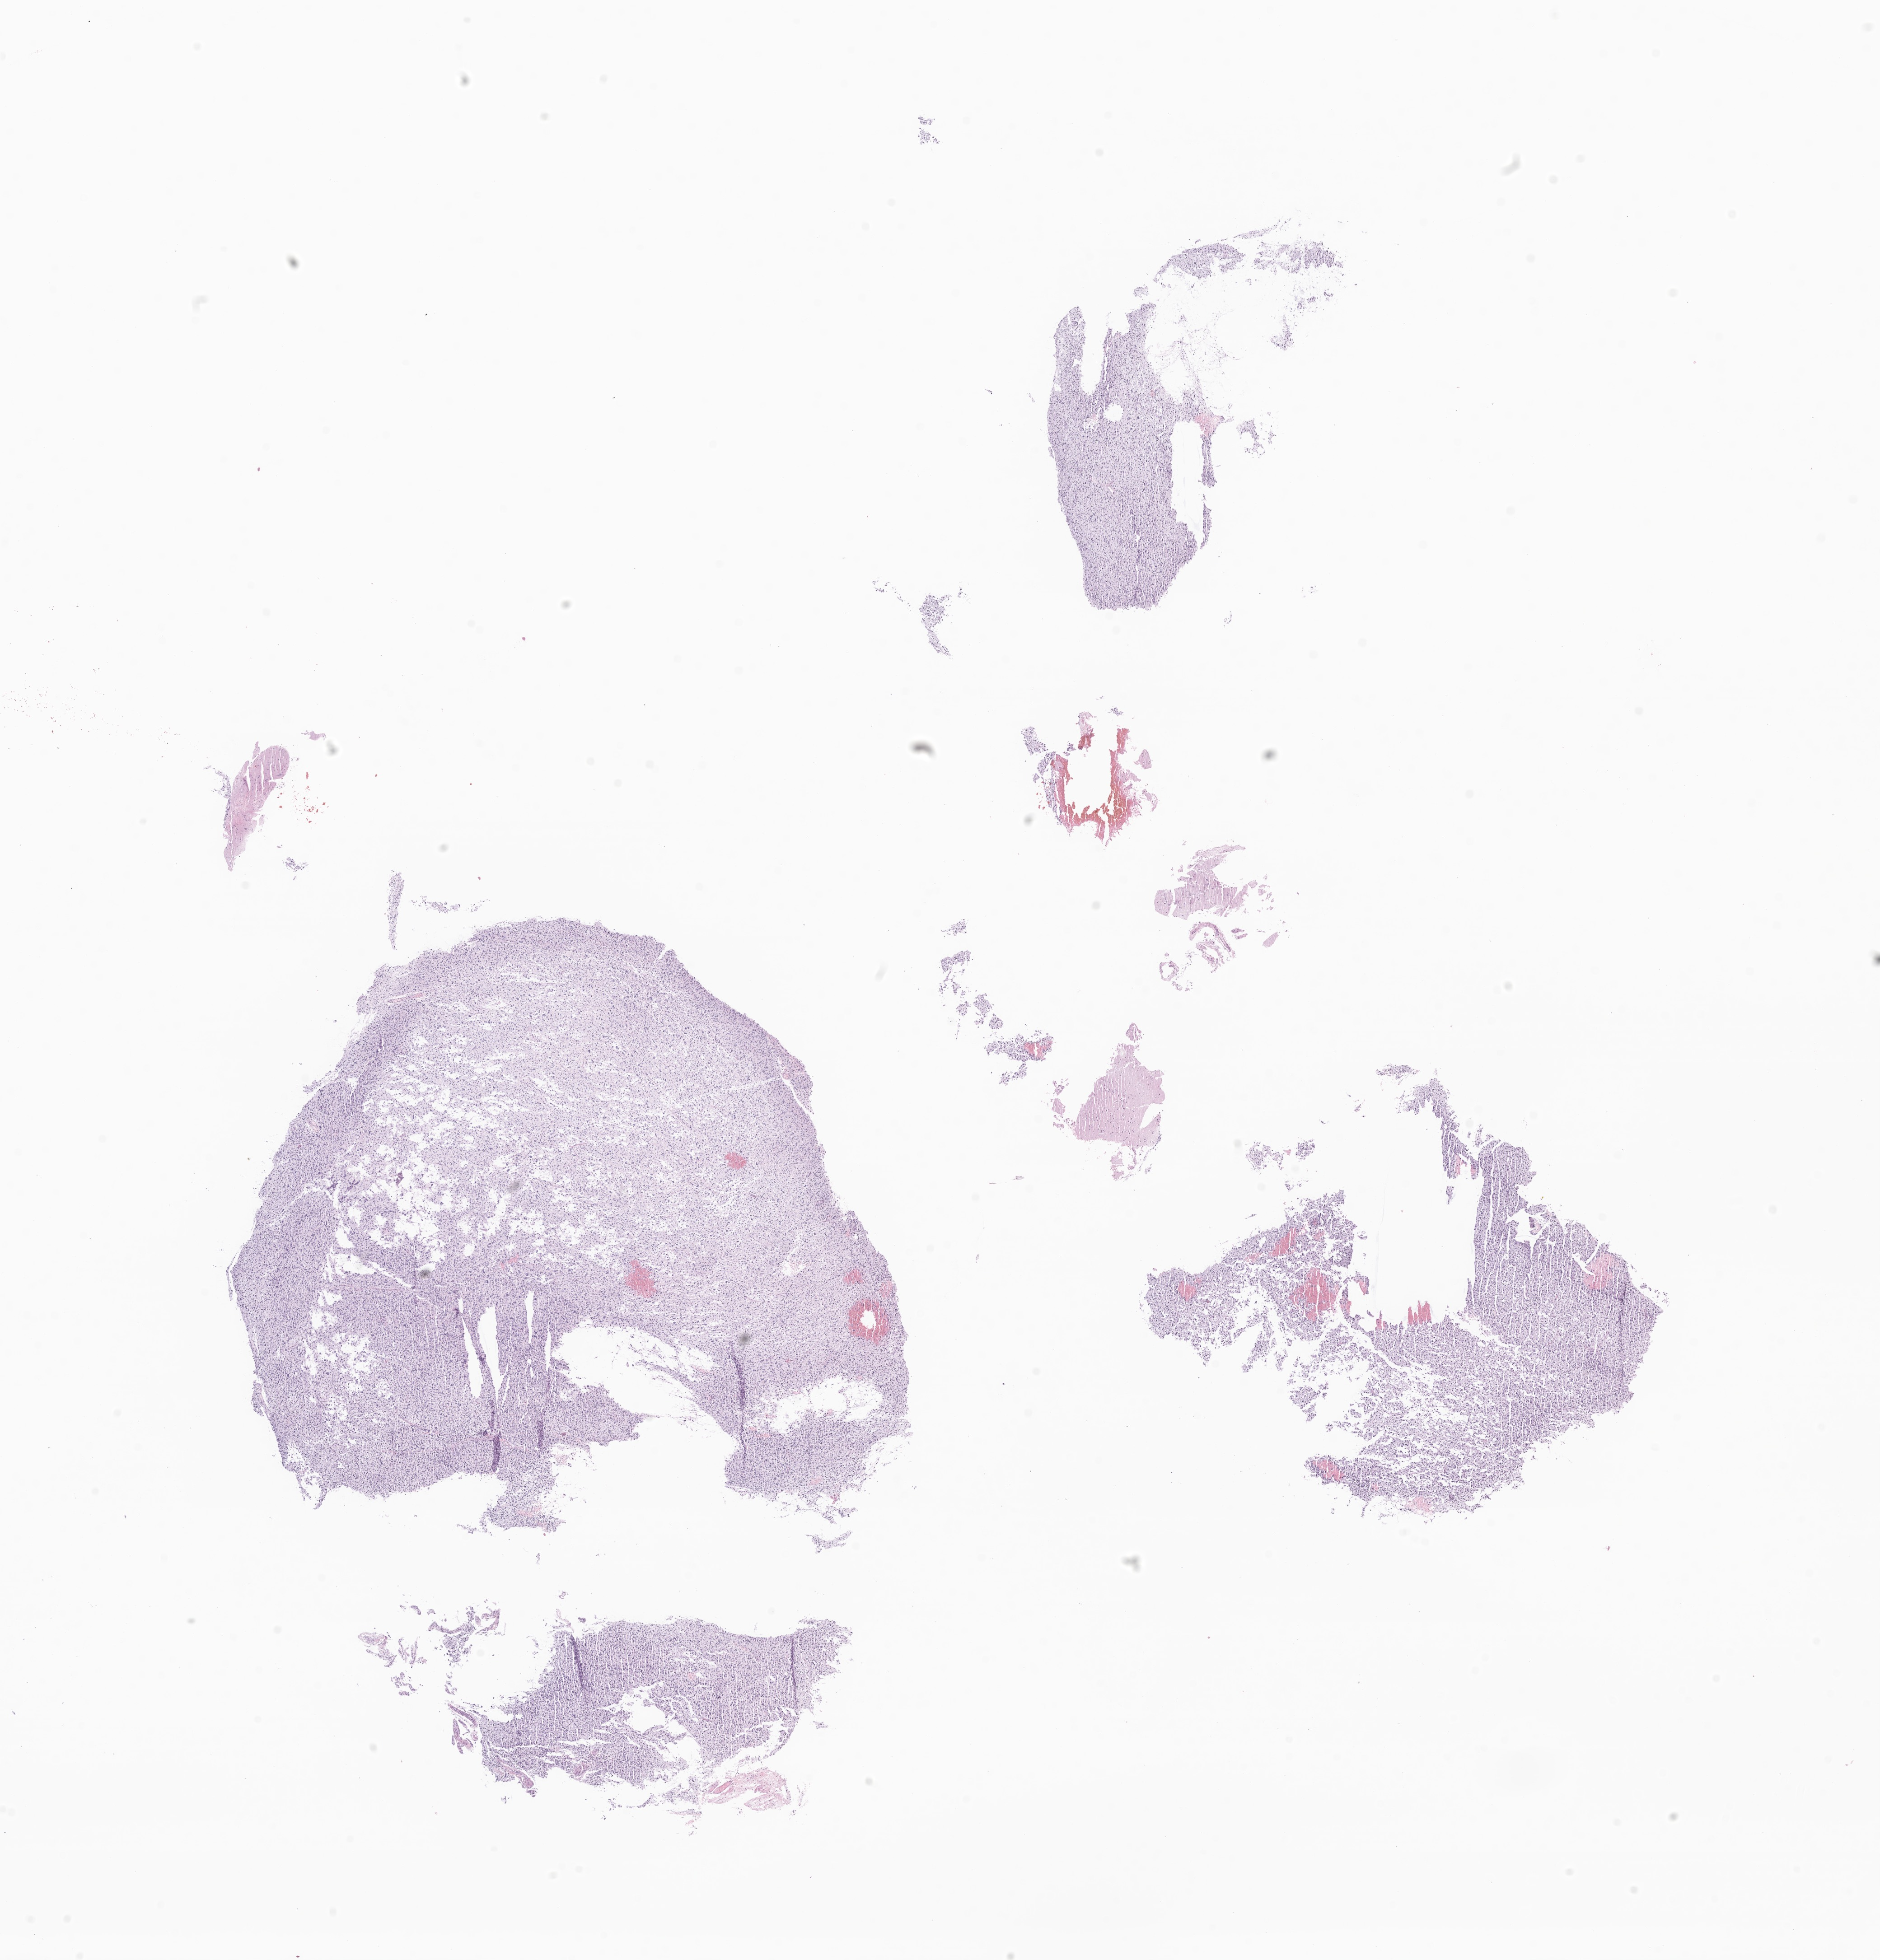
Whole-slide image, hematoxylin and eosin (H&E) stain of tumor tissue from the brain, low-resolution overview of the scanned area, about 17.5 x 18.3 mm, formalin-fixed paraffin-embedded section. Female patient, age 198 months (16 years 6 months).
- diagnosis (ICD-O-3 morphology term): Glioma, malignant